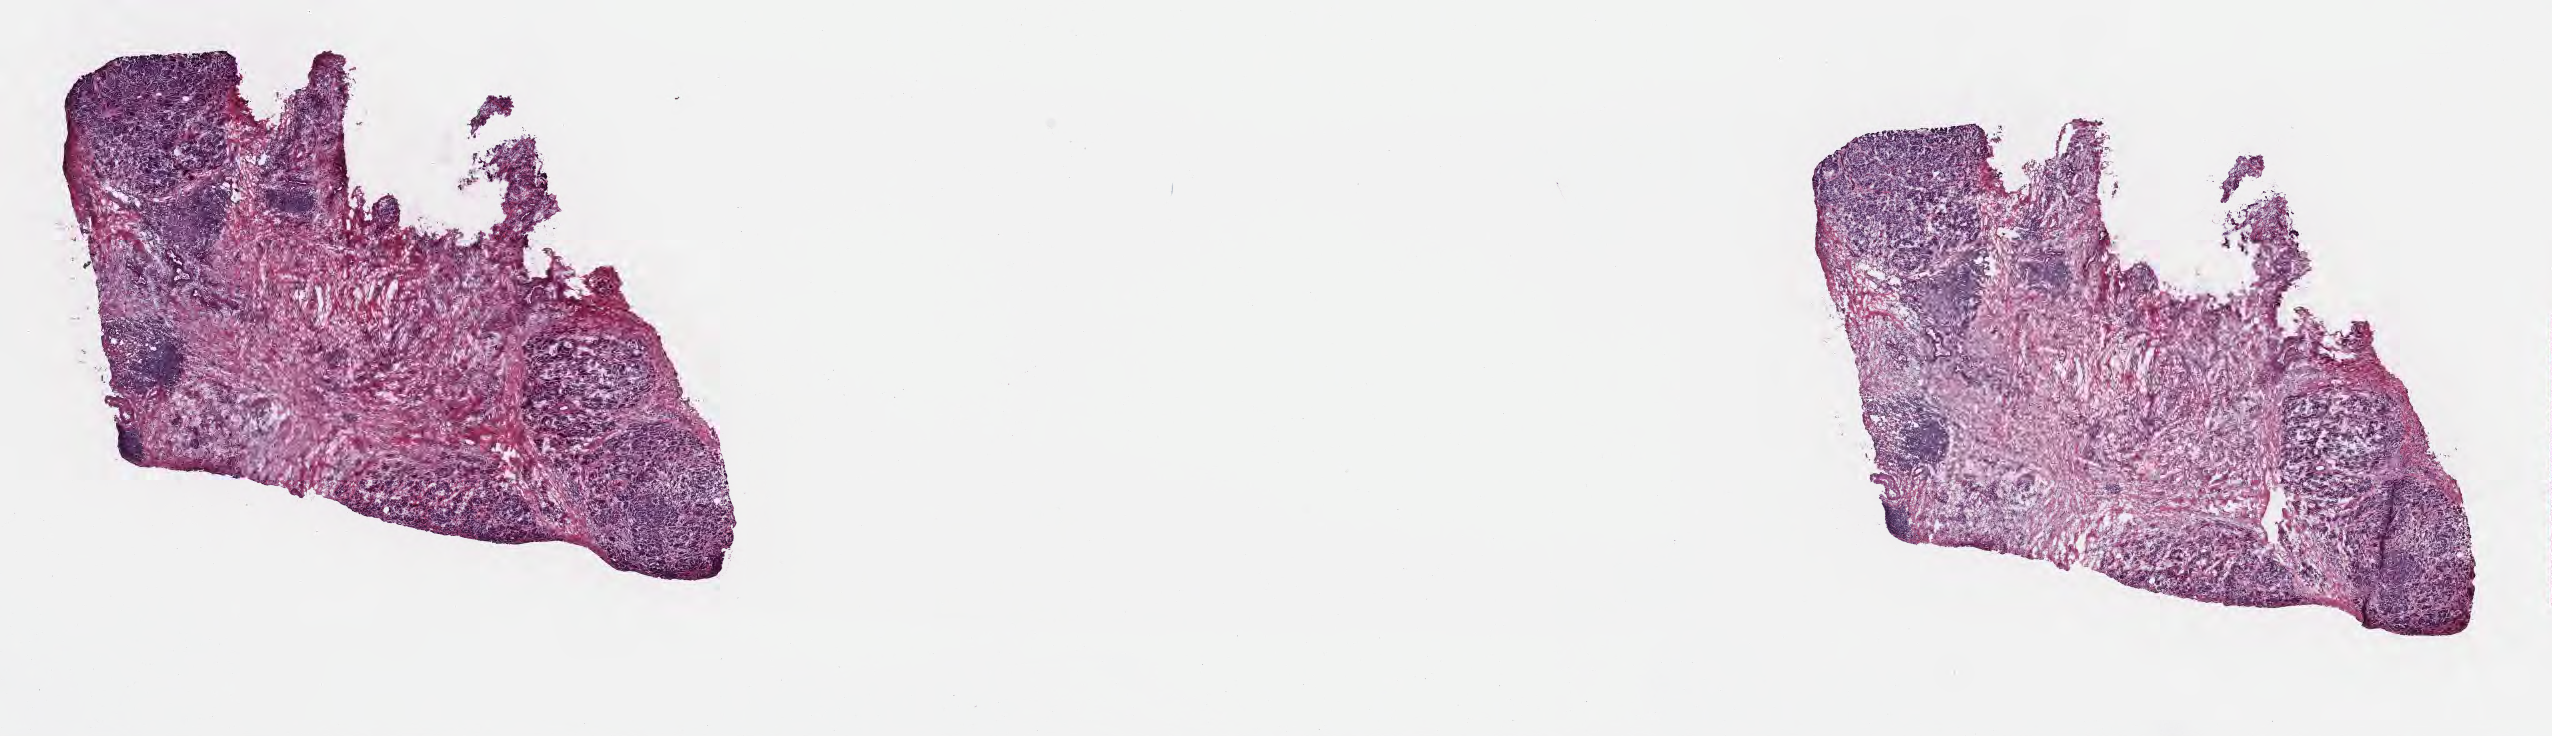
Digitized haematoxylin and eosin-stained section — shown as a low-resolution overview of the whole scanned area (about 20.6 x 6.0 mm); frozen section; primary tumor; anatomic site: head of pancreas. Patient: male, age at initial diagnosis 77 years. Tumor grade: G2 (moderately differentiated). Pathologist review of this section (percent, as recorded): tumor cells 10%, tumor nuclei 50%, stromal cells 65%, necrosis 0%, normal cells 25%. Inflammatory infiltration, as recorded: lymphocyte infiltration 0%, monocyte infiltration 0%, neutrophil infiltration 0%.
- diagnosis: Infiltrating duct carcinoma, NOS
- AJCC pathologic stage: Stage III